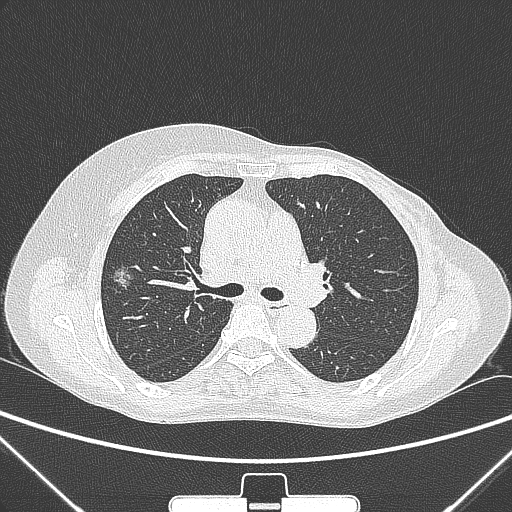
Chest CT, one axial slice. Slice 160 of 265 in the series (ordered by position). 120 kVp. Lung window (W 1500 / L -600 HU). 1 mm slice thickness. 512 × 512 image matrix, field of view 350 × 350 mm. Patient: female, 64 years. Case-level facts recorded for this patient, not image findings: clinical TNM (as recorded): T1c N0 M0.
Structures marked on this image (rectangle marked by the reading radiologist):
- lung tumour (recorded histology: adenocarcinoma): bounding box (x1, y1, x2, y2) in pixels: (104, 263, 142, 301)